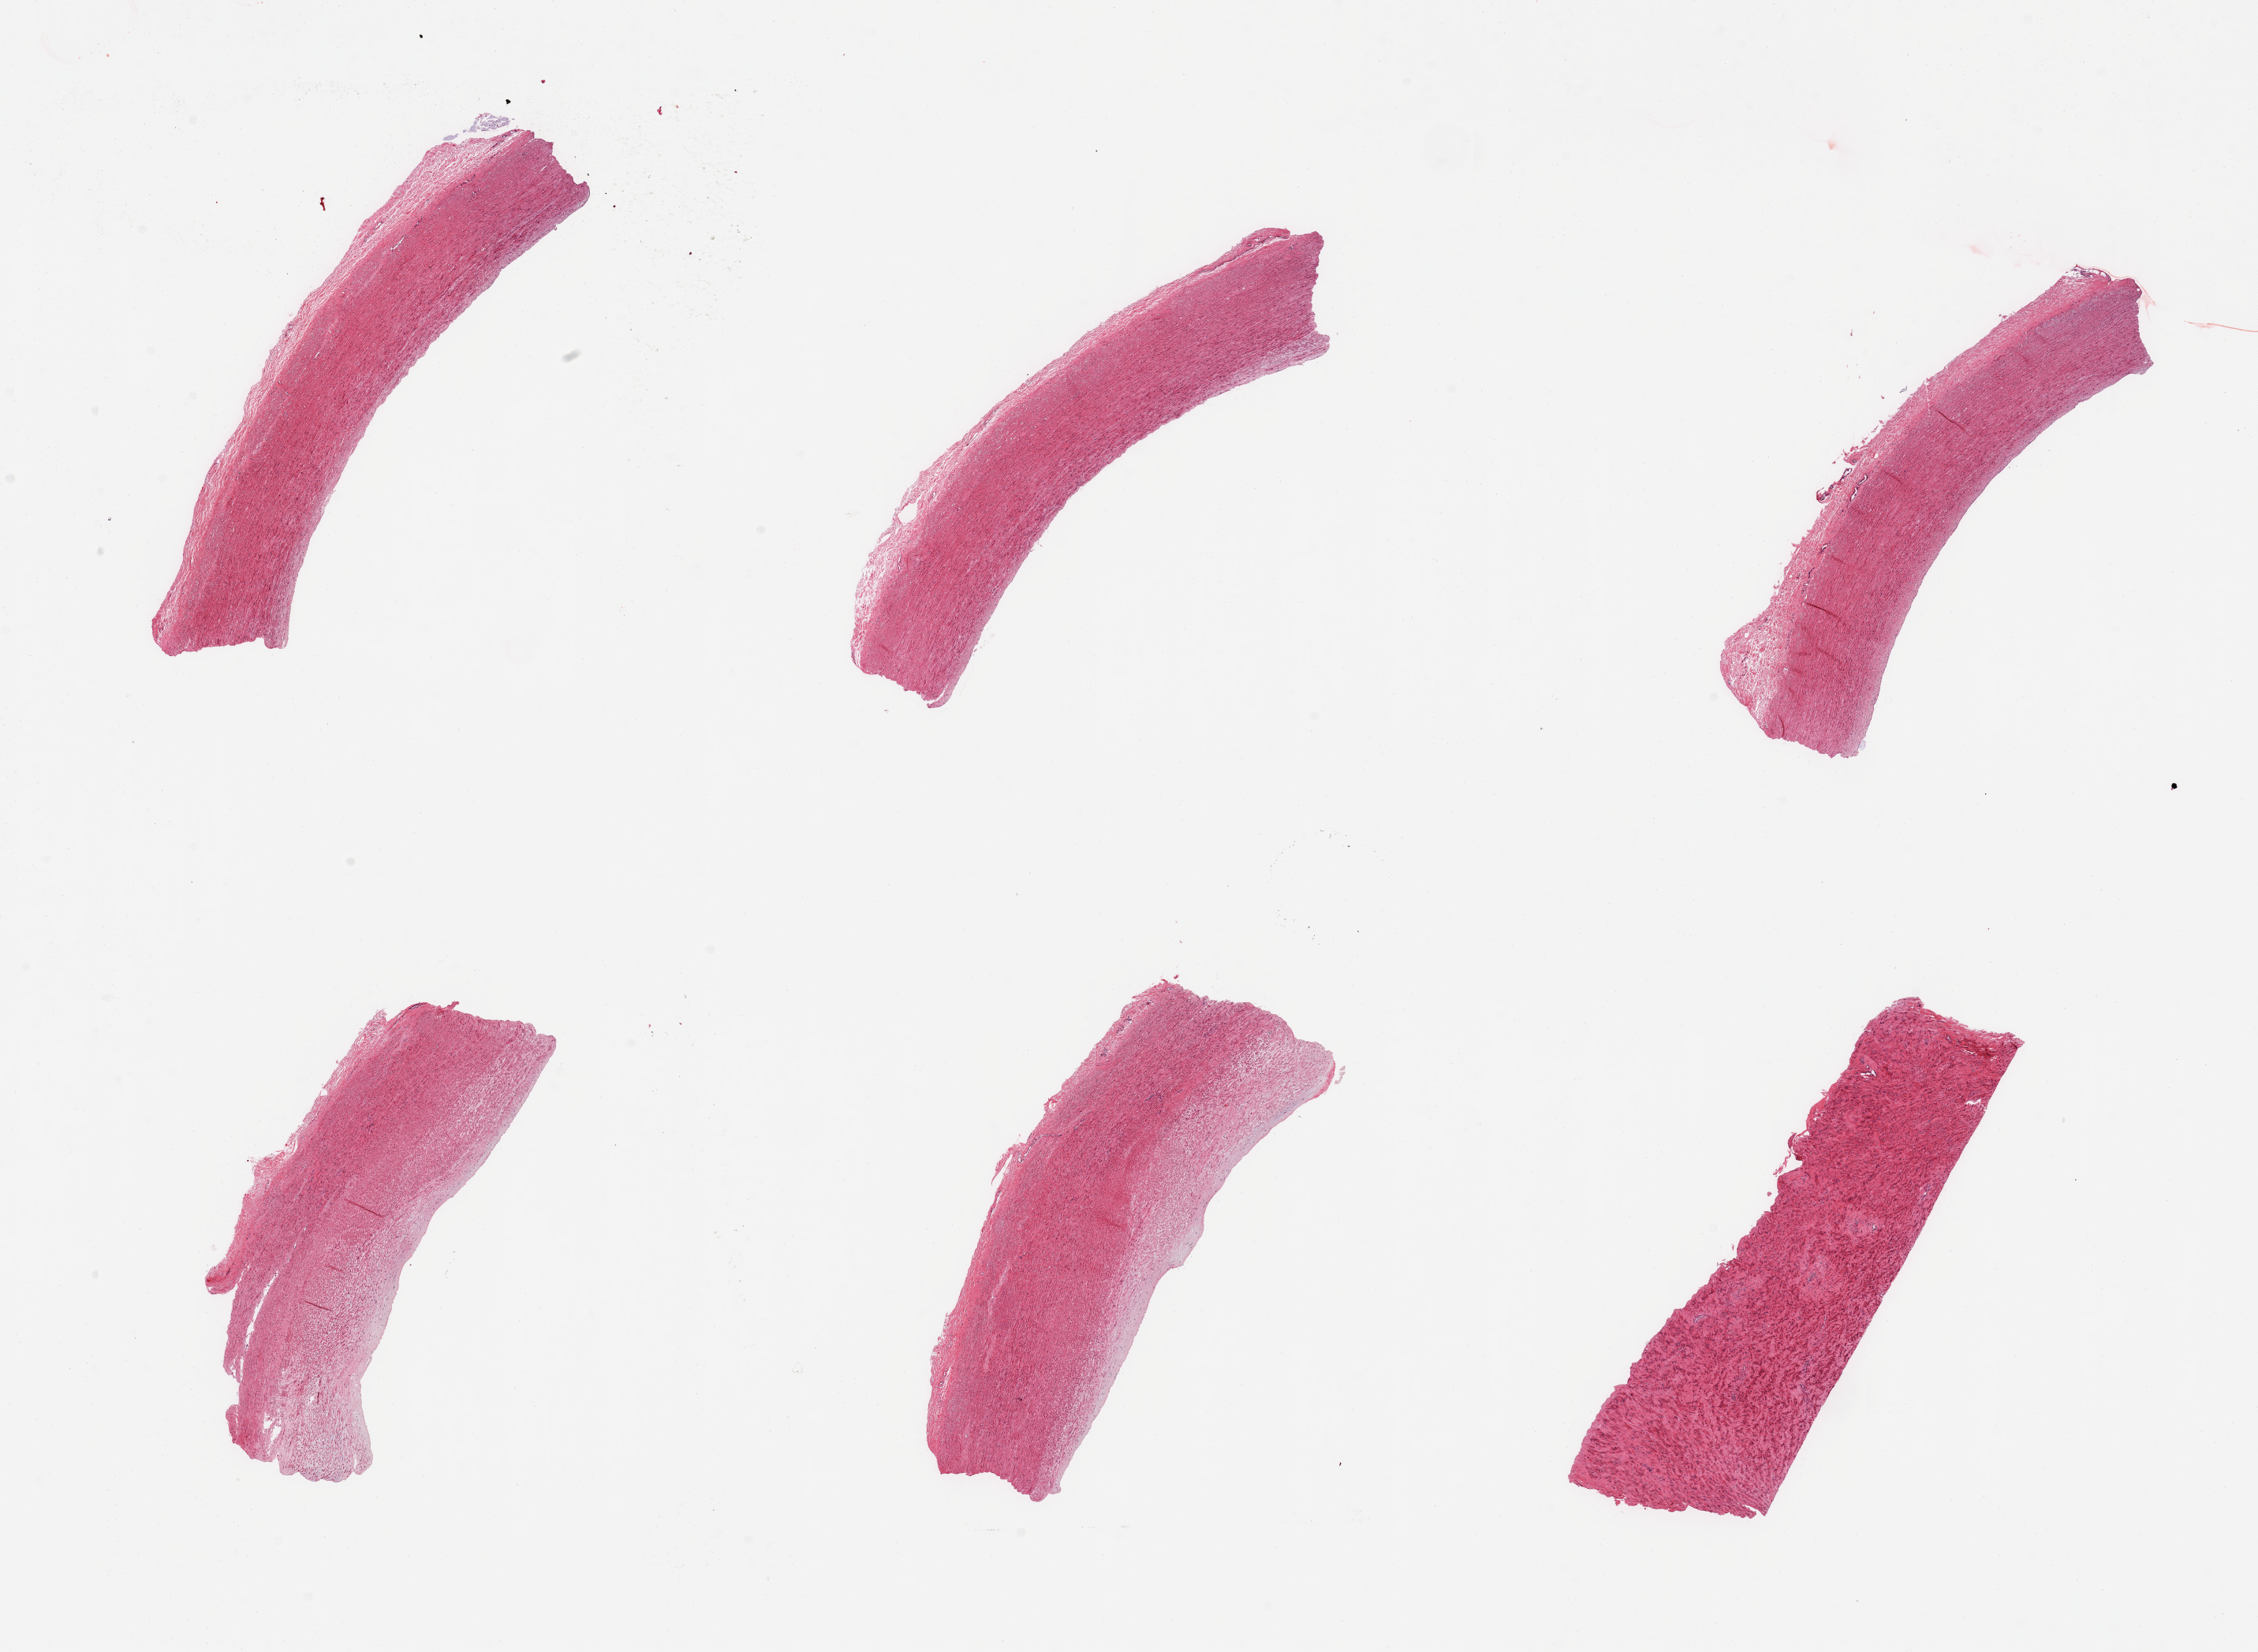
H&E whole-slide image, brightfield — whole scanned area (about 22.6 x 16.6 mm, acquisition: 20x scan) shown as a low-resolution overview. PAXgene-fixed paraffin-embedded (PFPE) section. Section of aorta (target tissue). Tissue donor sample. Male donor.
Pathologist's review note for this sample: 6 pieces, atherosis up to ~0.7mm.